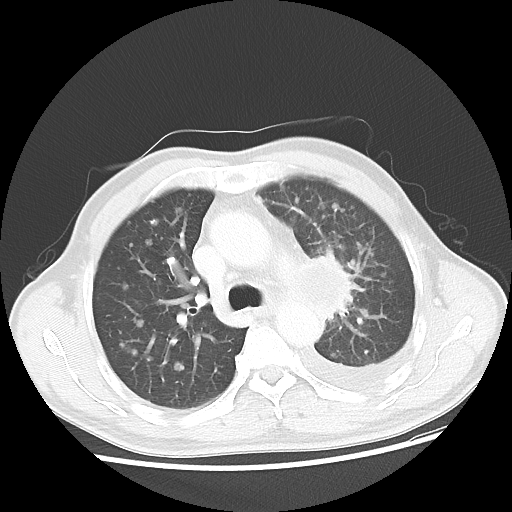
Chest CT, one axial slice; slice 31 of 47 in the series (ordered by position); lung window (W 1500 / L -600 HU); 5 mm slice thickness; 512 × 512 image matrix, field of view 362 × 362 mm. Male patient, age 55 years. From the clinical record (not read from this slice): clinical TNM (as recorded): T2 N3 M1a.
Structures marked on this image (rectangle marked by the reading radiologist):
- lung tumour (recorded histology: squamous cell carcinoma): bounding box <313,249,379,356> (left, top, right, bottom; pixels)